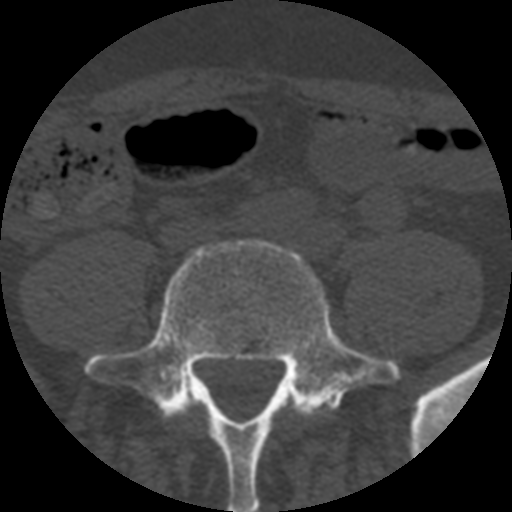
CT including the spine, one axial slice; slice 68 of 508 in the series (ordered by position); 120 kVp; bone window (W 1800 / L 400 HU); 1.25 mm slice thickness; 512 × 512 image matrix, field of view 160 × 160 mm. Patient age 57 years. Case-level facts recorded for this patient, not image findings: primary cancer: prostate.
Annotated regions visible in this slice (semi-automatic segmentation, software-assisted and operator-edited):
- L4 vertebra: bounding box (x1, y1, x2, y2) in pixels: (194, 401, 206, 409)
- L5 vertebra: (84, 240, 401, 512)